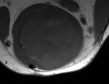
MRI of an extremity soft-tissue mass, one axial slice; position 29 of 50 along the scan axis; MR volume resampled by the dataset authors to the PET/CT grid (not the native acquisition matrix); 3.27 mm slice thickness; 109 × 84 image matrix, field of view 106 × 82 mm. Male patient. Case-level facts recorded for this patient, not image findings: histological type: synovial sarcoma; site of the primary tumour: left poplietal fossa.
Annotated regions visible in this slice (expert contour drawn on MRI and transferred to this co-registered scan by the dataset authors):
- gross tumour volume (mass): box from (x=14, y=14) to (x=85, y=70) px